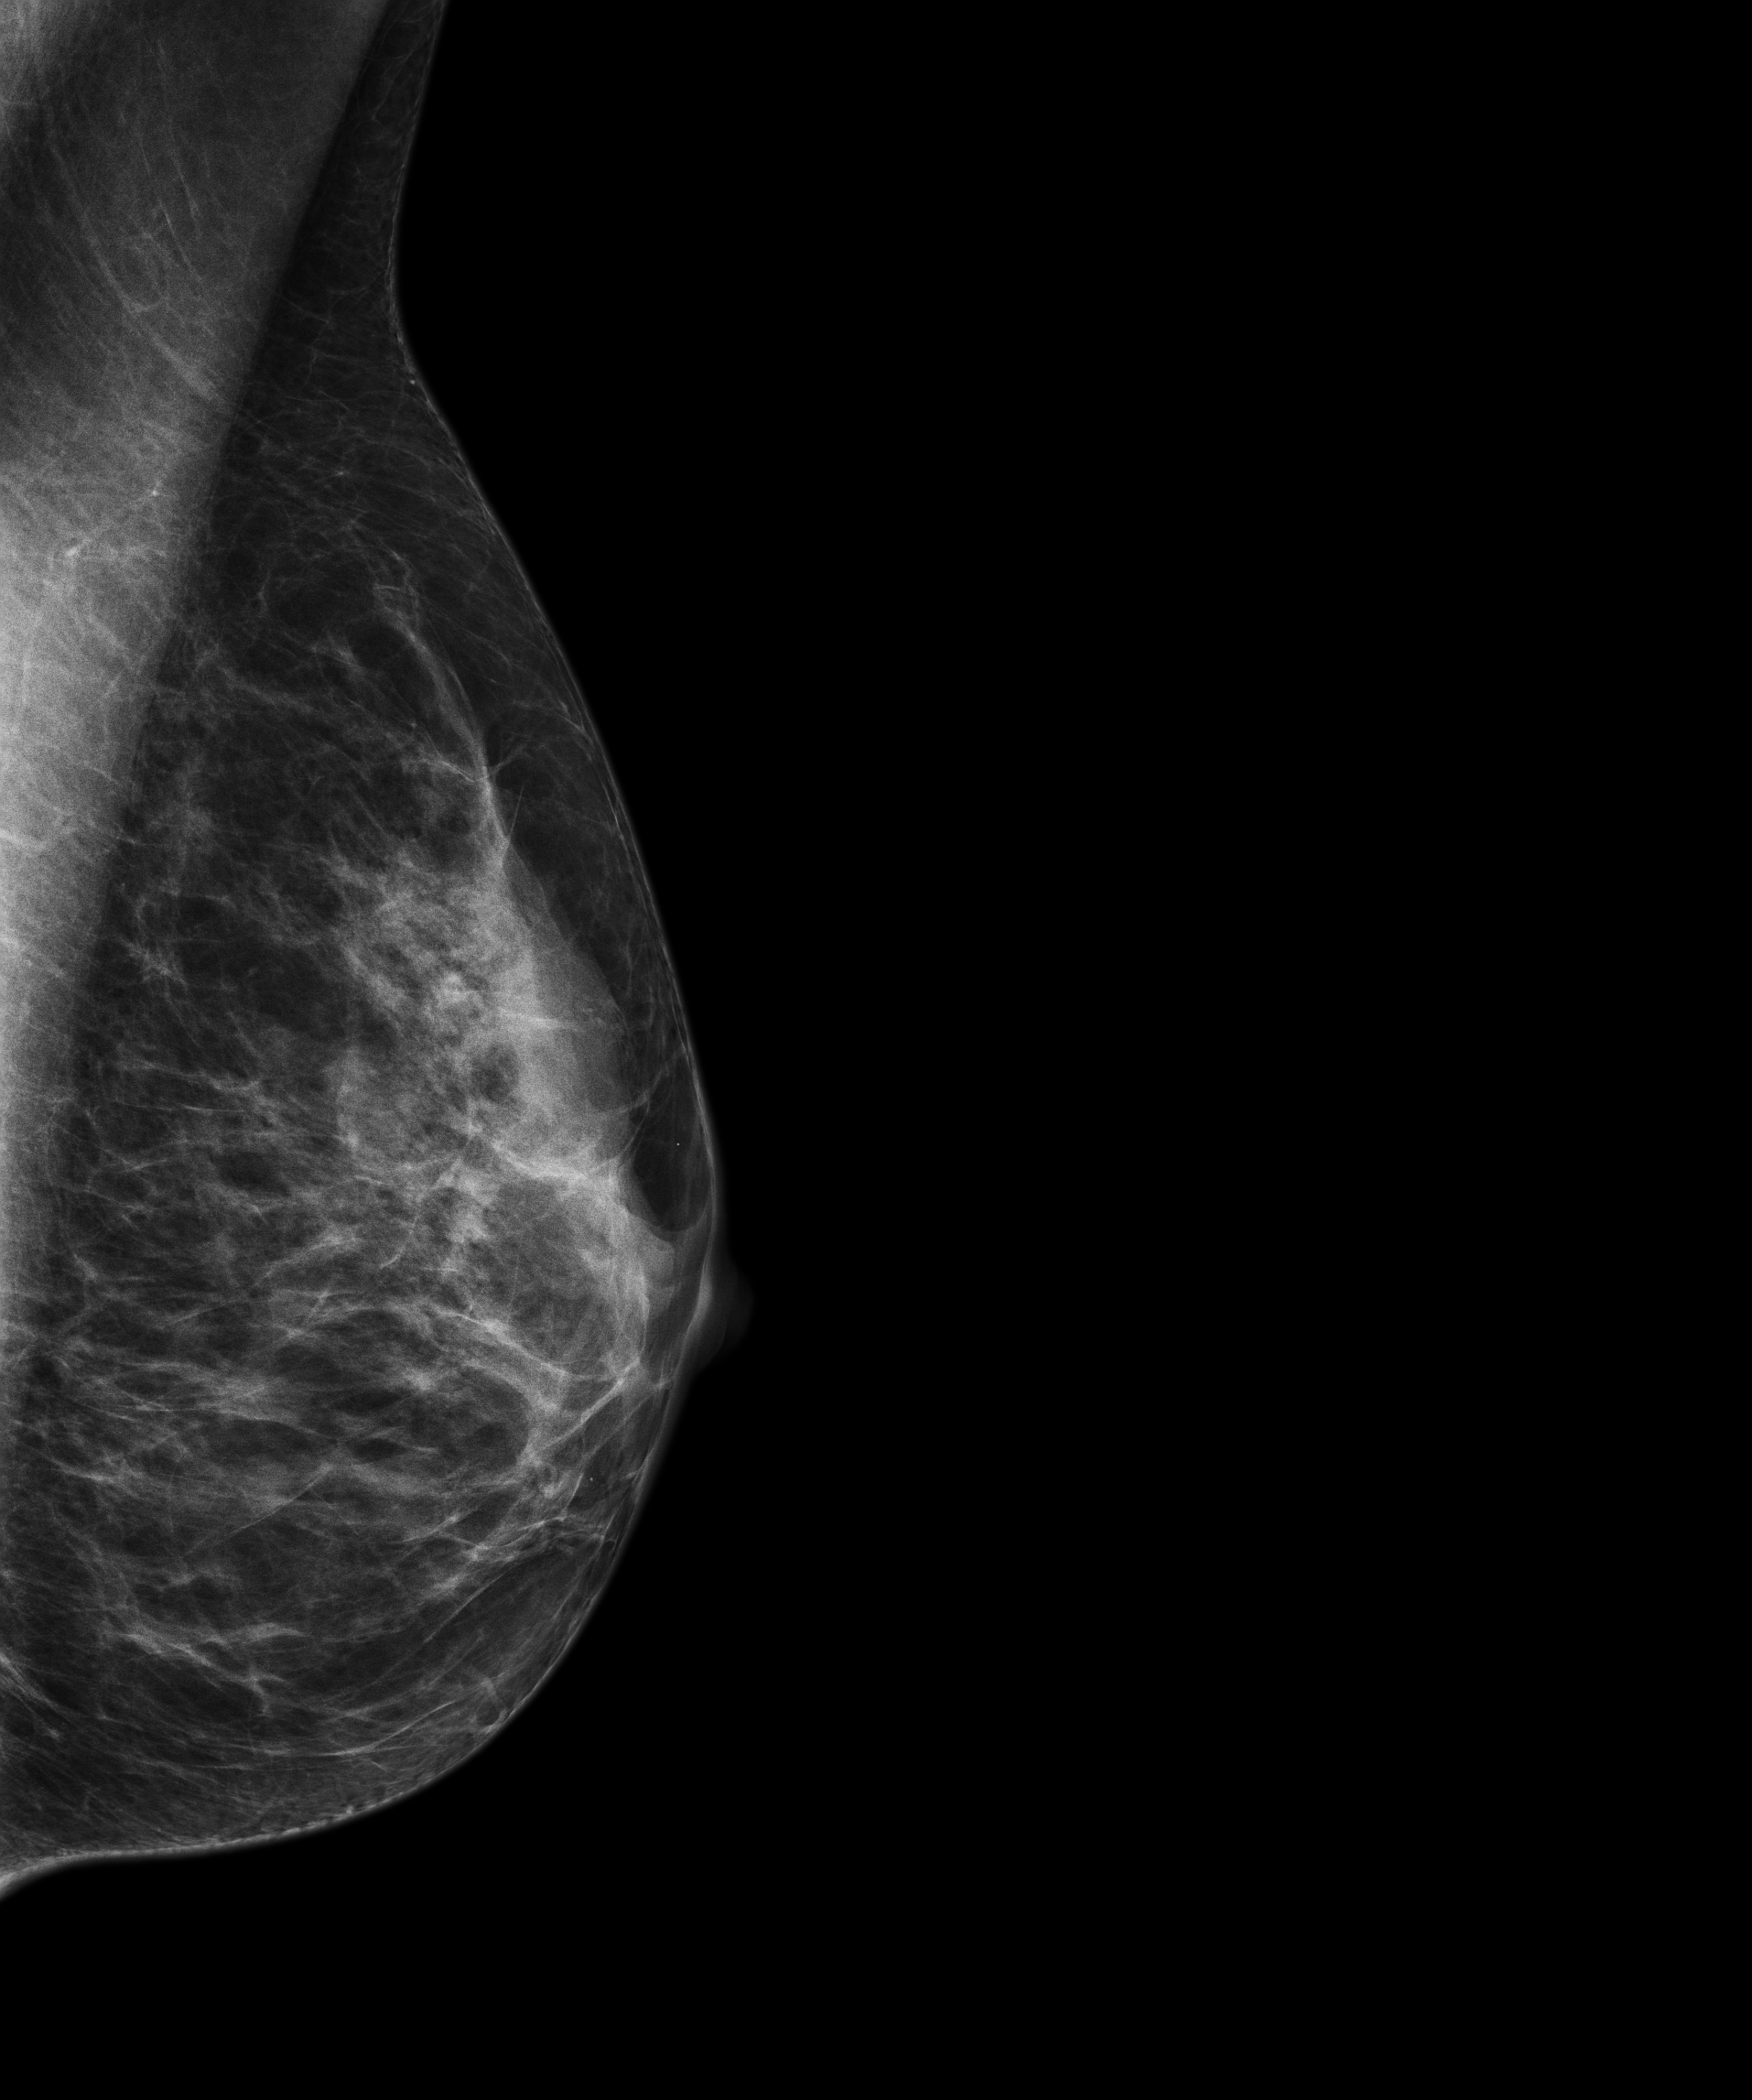
Full-field digital mammogram (FFDM), left breast, mediolateral oblique (MLO) view, annual screening mammography examination, compressed breast thickness 38 mm. Patient: female, 65 years.
Breast density at the screening exam (both breasts): heterogeneously dense (BI-RADS density category c). Final BI-RADS assessment for this screening round (tomosynthesis exam, both breasts): category 1. Recall: no recall after this screen.